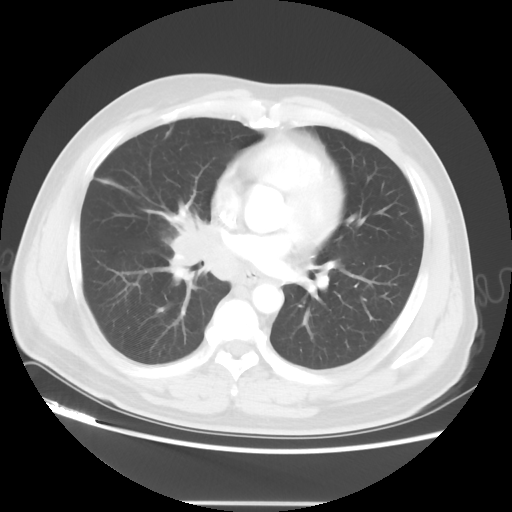
Chest CT, one axial slice. Slice 22 of 48 in the series (ordered by position). Reconstruction kernel STANDARD. 120 kVp. Lung window (W 1500 / L -600 HU). 5 mm slice thickness. 512 × 512 image matrix, field of view 390 × 390 mm. Patient: male, 53 years. From the clinical record (not read from this slice): clinical TNM (as recorded): T2 N3 M0.
Annotated regions visible in this slice (bounding box drawn by a radiologist):
- lung tumour (recorded histology: small cell carcinoma): box from (x=161, y=200) to (x=210, y=281) px